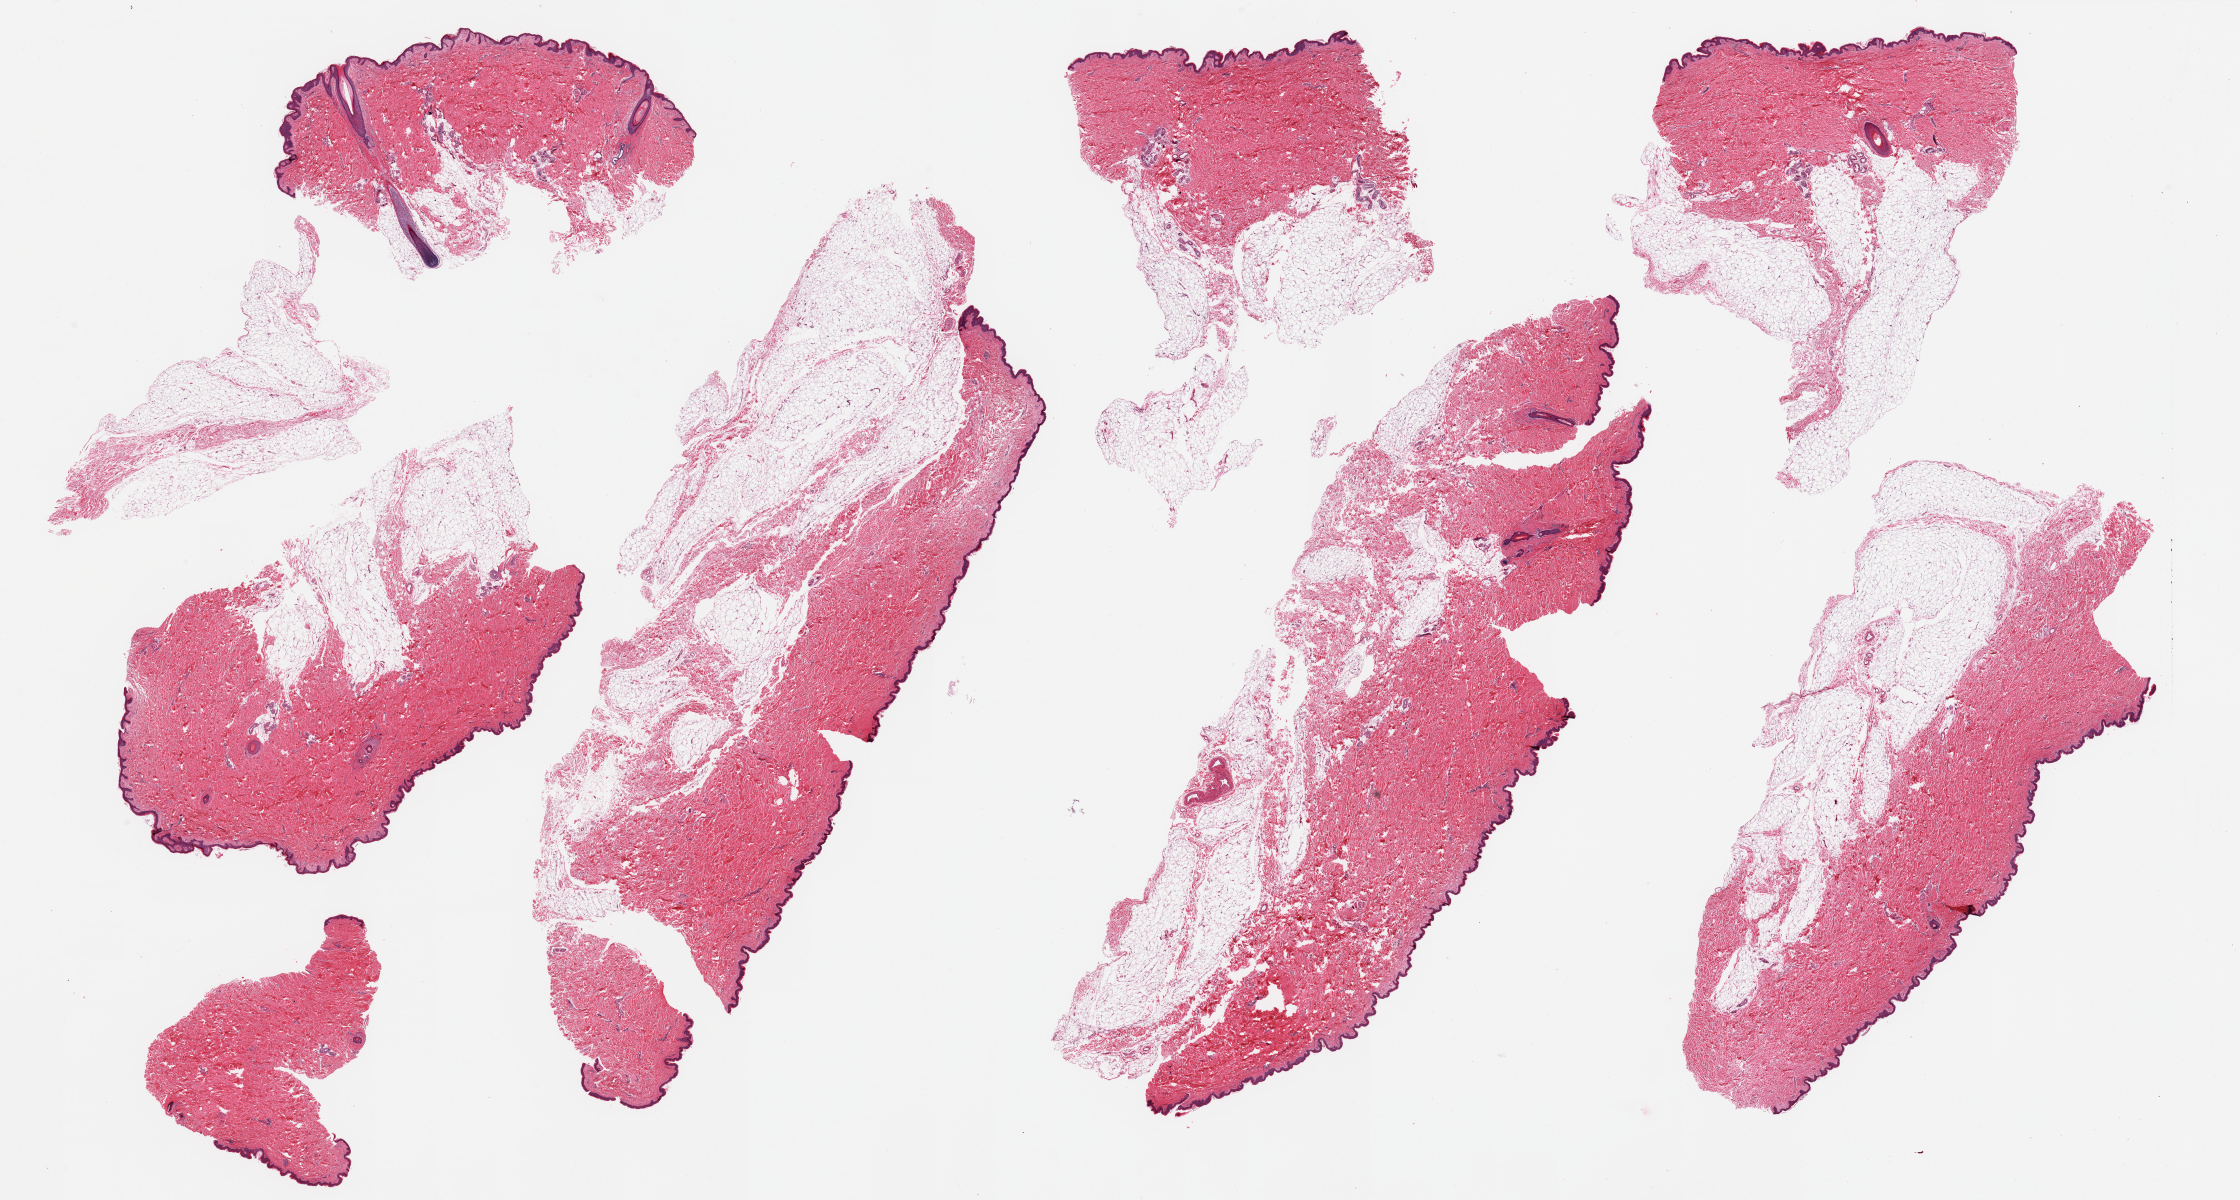
Digitized hematoxylin and eosin (H&E)-stained section — shown as a low-resolution overview of the whole scanned area (about 35.4 x 19.0 mm, acquisition: 20x scan). PAXgene-fixed, paraffin-embedded tissue. Target tissue: skin of suprapubic region. Tissue donor sample. Female donor.
- pathologist's review note for this sample: 7 pieces (fragmented), squamous epithelium is ~30-40 microns; abundant dermal fat up to ~5mm